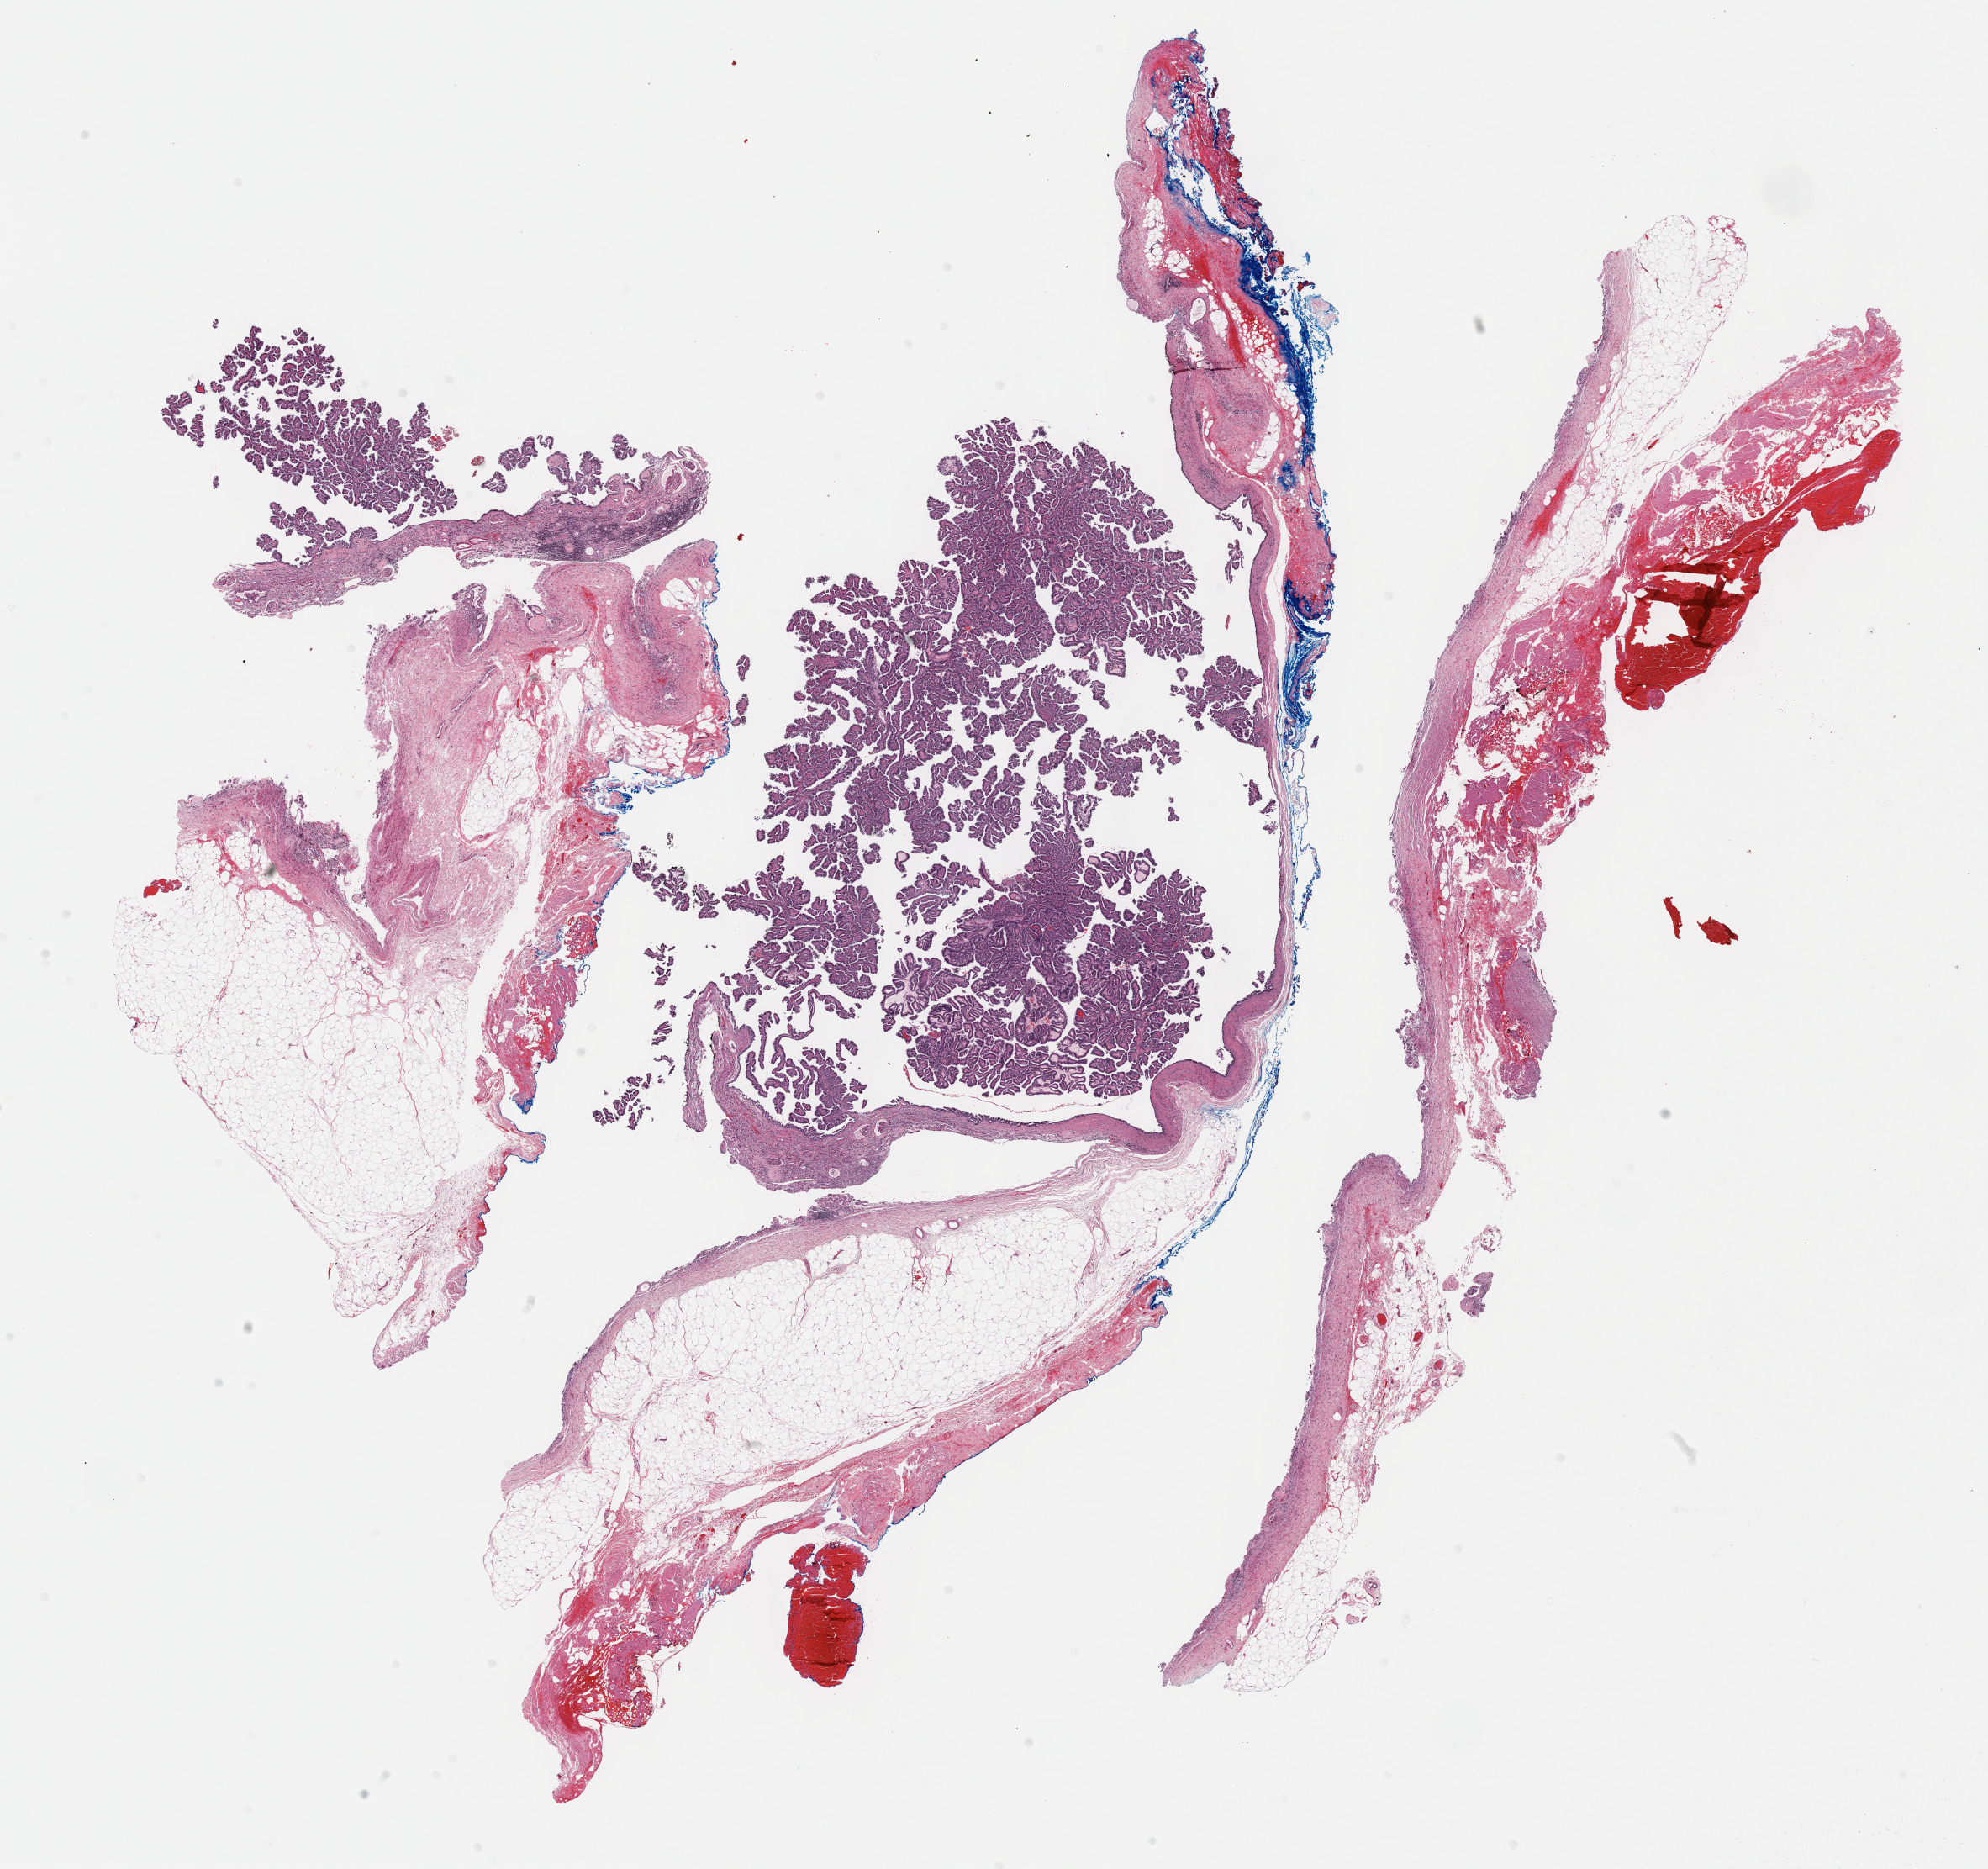
H&E-stained whole-slide image — whole scanned area (about 19.1 x 18.0 mm, acquisition: 40x scan) shown as a low-resolution overview. Formalin-fixed paraffin-embedded (FFPE) diagnostic section. Kidney, primary tumour sample. Patient: female, age at initial diagnosis 57 years.
Pathologic diagnosis: Papillary adenocarcinoma, NOS.